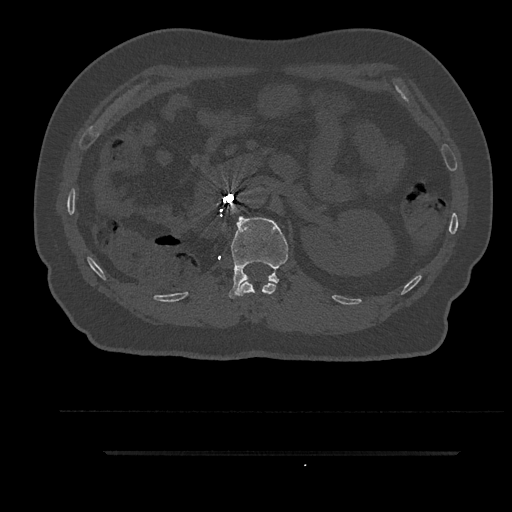
CT including the spine, one axial slice. Slice 196 of 797 in the series (ordered by position). Reconstruction kernel Br40s/3. Bone window (W 1800 / L 400 HU). 0.5 mm slice thickness. 512 × 512 image matrix, field of view 432 × 432 mm. Patient: male, 63 years. Case-level facts recorded for this patient, not image findings: primary cancer: renal.
Annotated regions visible in this slice (semi-automatic segmentation, software-assisted and operator-edited):
- L1 vertebra: box from (x=228, y=216) to (x=289, y=299) px
- T12 vertebra: (x=238, y=280)–(x=276, y=296)